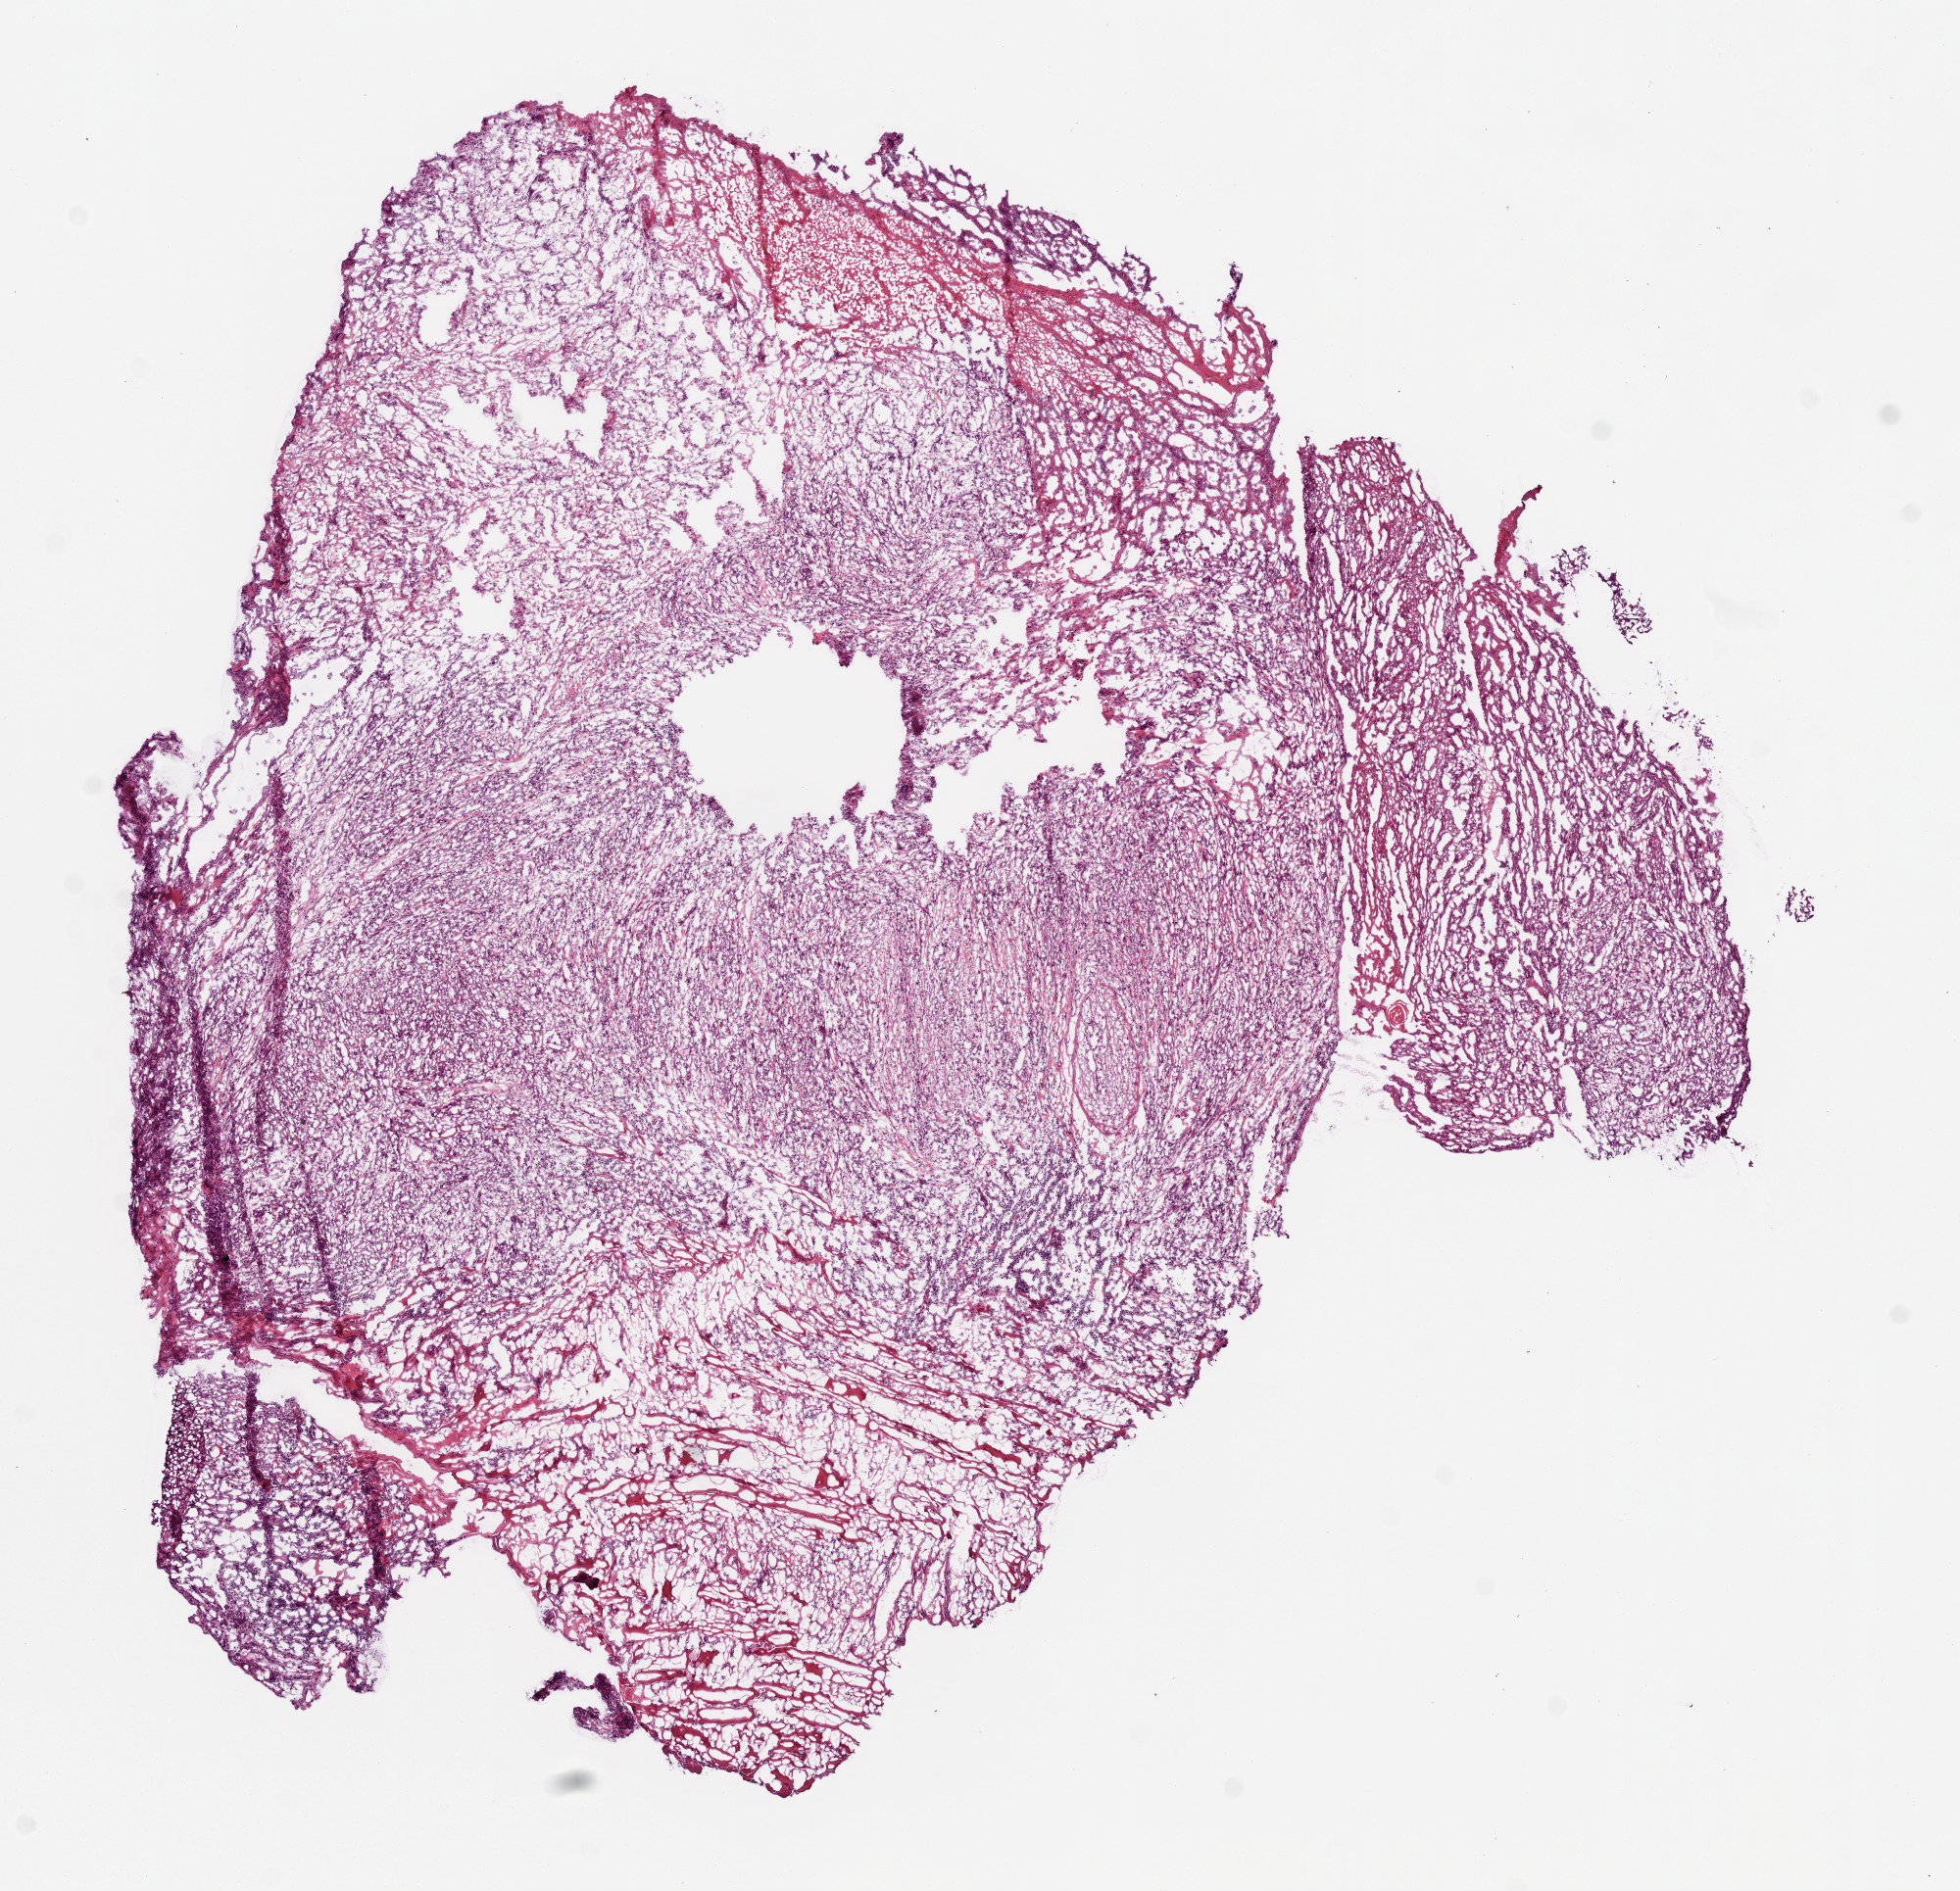
Whole-slide histology image, Hematoxylin and eosin (H&E) stained — a low-resolution overview of the entire scanned area, about 8.0 x 7.7 mm; frozen section; primary tumour sample from the head and neck. Male patient; age at initial diagnosis 48 years. Slide review estimates, as recorded: tumour cells 90%, tumour nuclei 70%.
Histologic diagnosis: Squamous cell carcinoma, NOS (larynx, NOS).